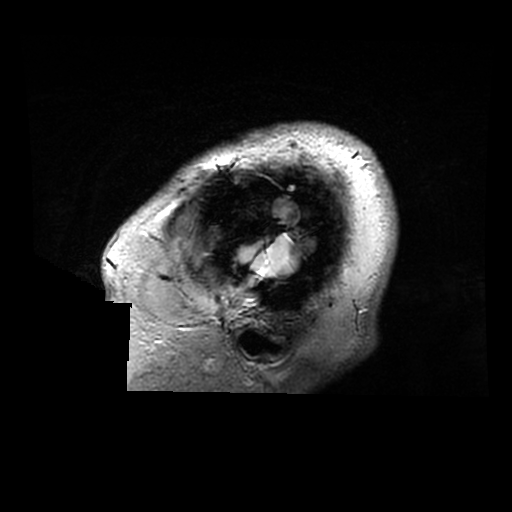
Brain MRI from a brain-tumour surgery series, one sagittal slice. Slice 263 of 320 in the series (ordered by position). 0.6 mm slice thickness. 512 × 512 image matrix, field of view 240 × 240 mm. Case-level facts recorded for this patient, not image findings: histopathology: Astrocytoma; WHO grade: 2; IDH mutation: yes.
Annotated regions visible in this slice (outlined manually by an expert reader):
- tumour: box from (x=239, y=235) to (x=302, y=276) px